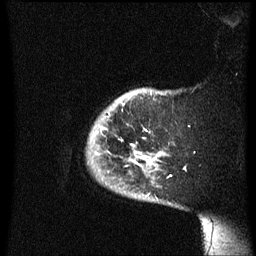
Breast MRI (dynamic contrast-enhanced), one sagittal slice. Slice 53 of 60 in the series (ordered by position). Dynamic contrast-enhanced series, image 2 of 3 at this slice position (ordered by acquisition). 1.5 T. TE 4.2 ms, TR 8.4 ms. 2.3 mm slice thickness. 256 × 256 image matrix, field of view 200 × 200 mm. Female patient, age 38 years. Case-level facts recorded for this patient, not image findings: setting: breast cancer imaged before/during neoadjuvant chemotherapy; receptor status: HER2-positive.
Annotated regions visible in this slice (semi-automatically segmented with operator editing):
- analysis volume of interest (the breast-tissue region the enhancement analysis was run in; not a lesion): box from (x=86, y=88) to (x=178, y=207) px
- tumour enhancement mask (voxels above the 70 % enhancement threshold inside the analysis volume of interest): (x=133, y=152)–(x=161, y=165)